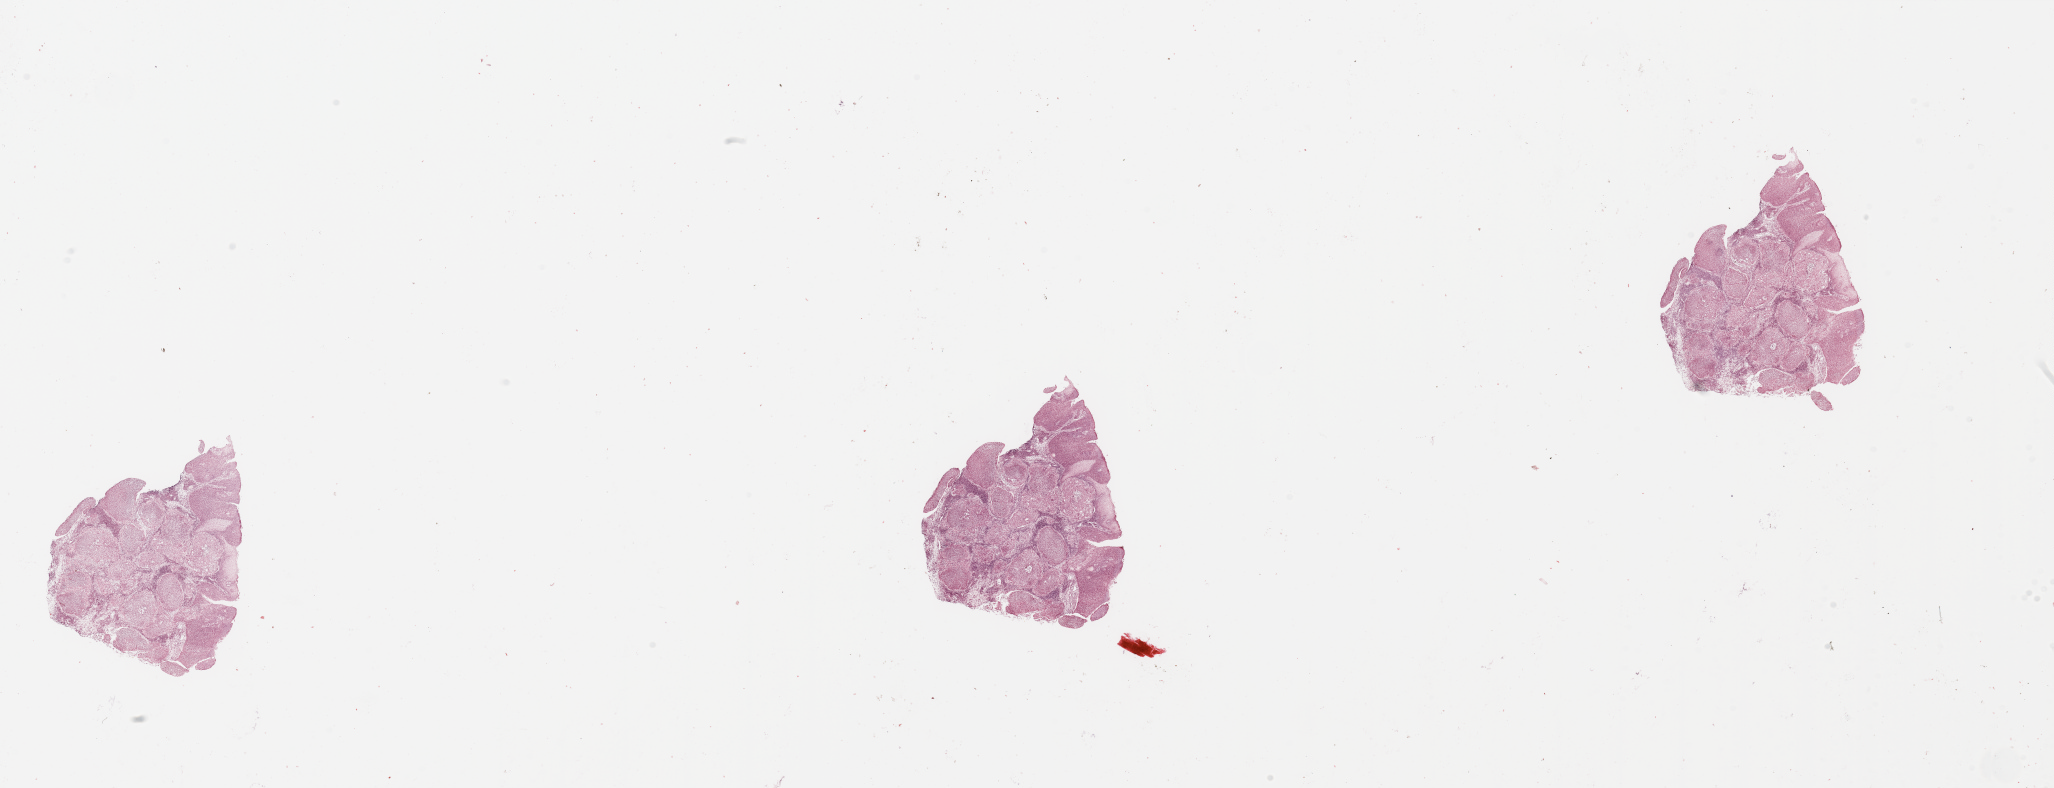
Whole-slide histology image, H&E, shown as a low-resolution overview of the whole scanned area (about 32.5 x 12.5 mm, slide scanned at 20x). Head and neck, tissue type not recorded. 63-year-old male patient.
Patient diagnosis: Squamous cell carcinoma, NOS (larynx, NOS).